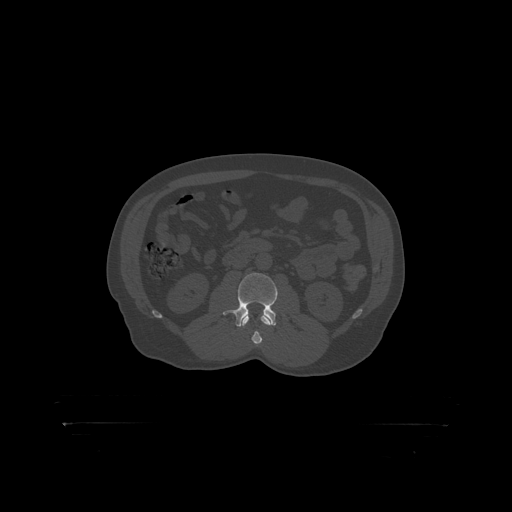
CT including the spine, one axial slice. Position 277 of 399 along the scan axis. Reconstruction kernel STANDARD. 120 kVp. Bone window (W 1800 / L 400 HU). 1.25 mm slice thickness. 512 × 512 image matrix. Patient: male, 46 years. Case-level facts recorded for this patient, not image findings: primary cancer: skin.
Annotated regions visible in this slice (semi-automatically segmented with operator editing):
- L2 vertebra: bounding box [x1, y1, x2, y2] px = [244, 315, 266, 319]
- L3 vertebra: [228, 273, 278, 319]